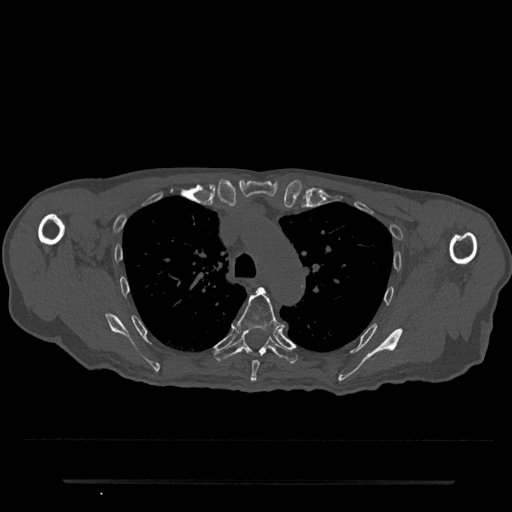
CT including the spine, one axial slice. Position 558 of 797 along the scan axis. Reconstruction kernel Br40s/3. 120 kVp. Bone window (W 1800 / L 400 HU). 0.5 mm slice thickness. 512 × 512 image matrix, field of view 427 × 427 mm. Patient: male, 74 years. From the clinical record (not read from this slice): primary cancer: prostate.
Annotated regions visible in this slice (semi-automatic segmentation, software-assisted and operator-edited):
- T5 vertebra: bounding box (x1, y1, x2, y2) in pixels: (237, 287, 285, 382)
- T6 vertebra: (214, 333, 298, 364)